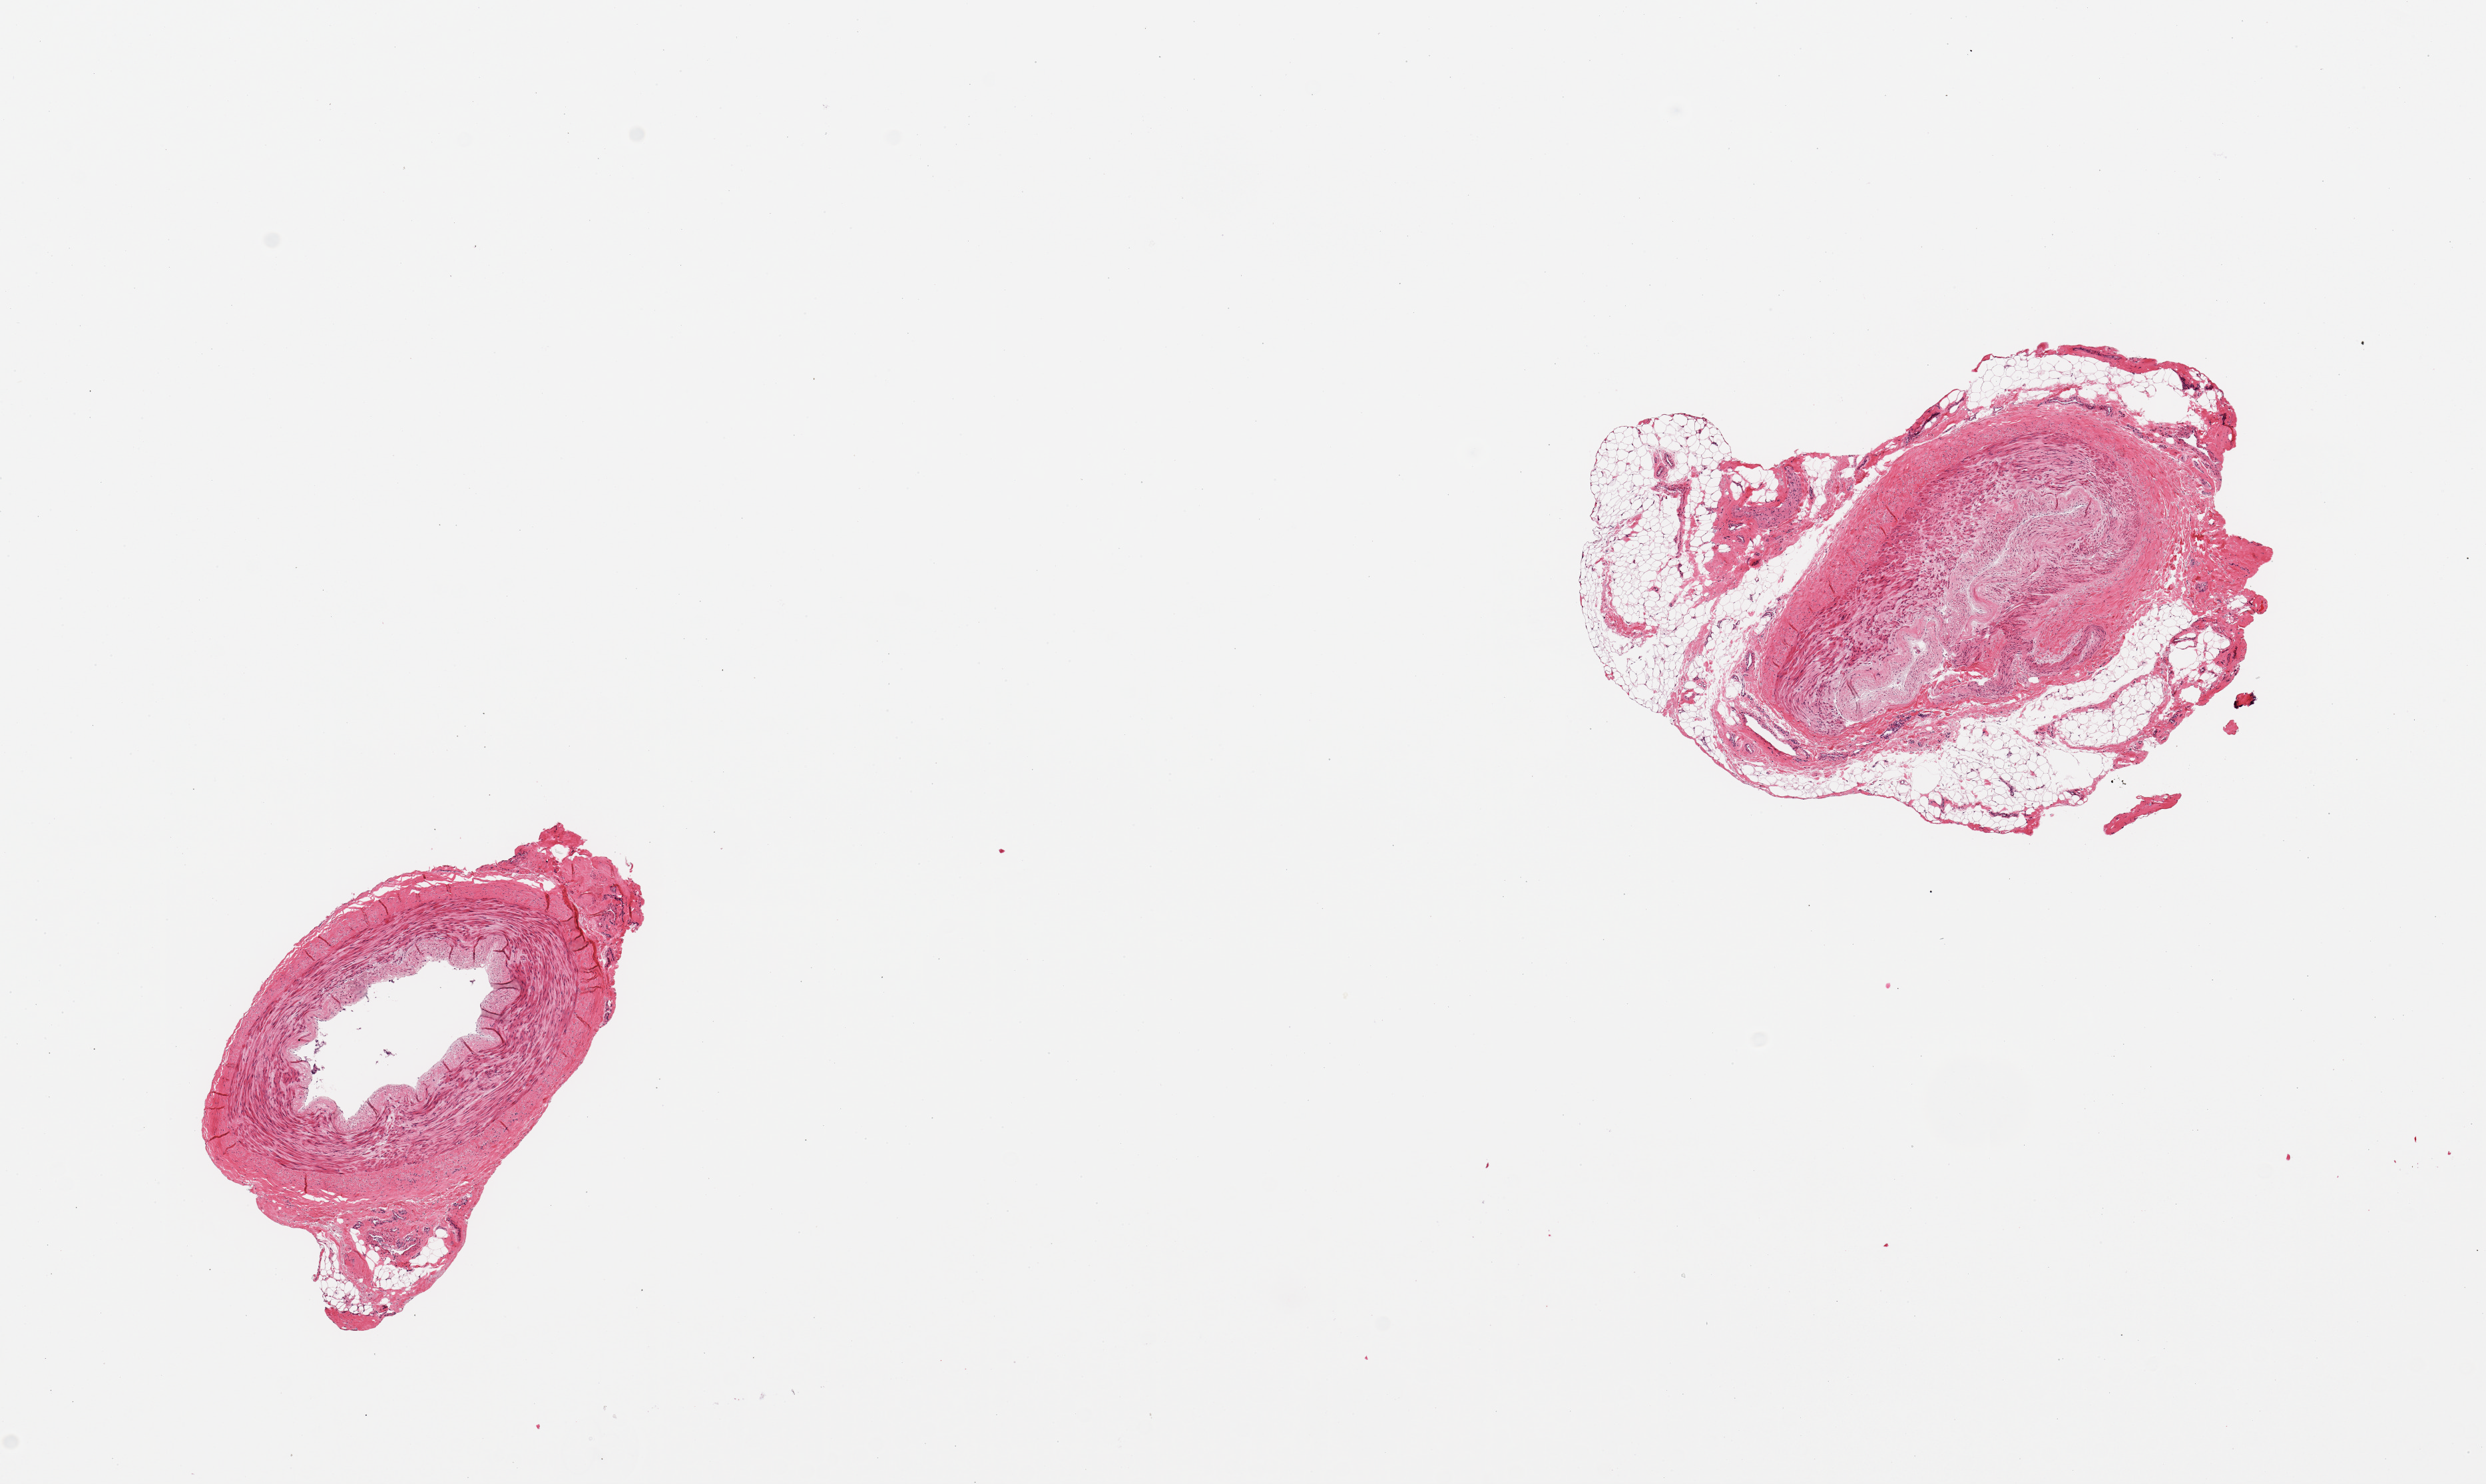
Whole-slide image, haematoxylin and eosin stain, shown as a low-resolution overview of the whole scanned area (about 14.8 x 8.8 mm), PAXgene-fixed, paraffin-embedded tissue, section of tibial artery (target tissue), tissue donor sample.
Review note (as recorded): 2 pieces; 1 piece has 40% untrimmed fat.